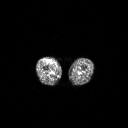
FDG PET of an extremity soft-tissue mass (from a PET/CT study), one axial slice; position 226 of 311 along the scan axis; 3.27 mm slice thickness; 128 × 128 image matrix, field of view 700 × 700 mm. Male patient, age 56 years. Case-level facts recorded for this patient, not image findings: histological type: pleiomorphic leiomyosarcoma; grade: intermediate; site of the primary tumour: right thigh.
Structures marked on this image (expert contour drawn on MRI and transferred to this co-registered scan by the dataset authors):
- gross tumour volume including surrounding oedema: bounding box <47,59,51,63> (left, top, right, bottom; pixels)